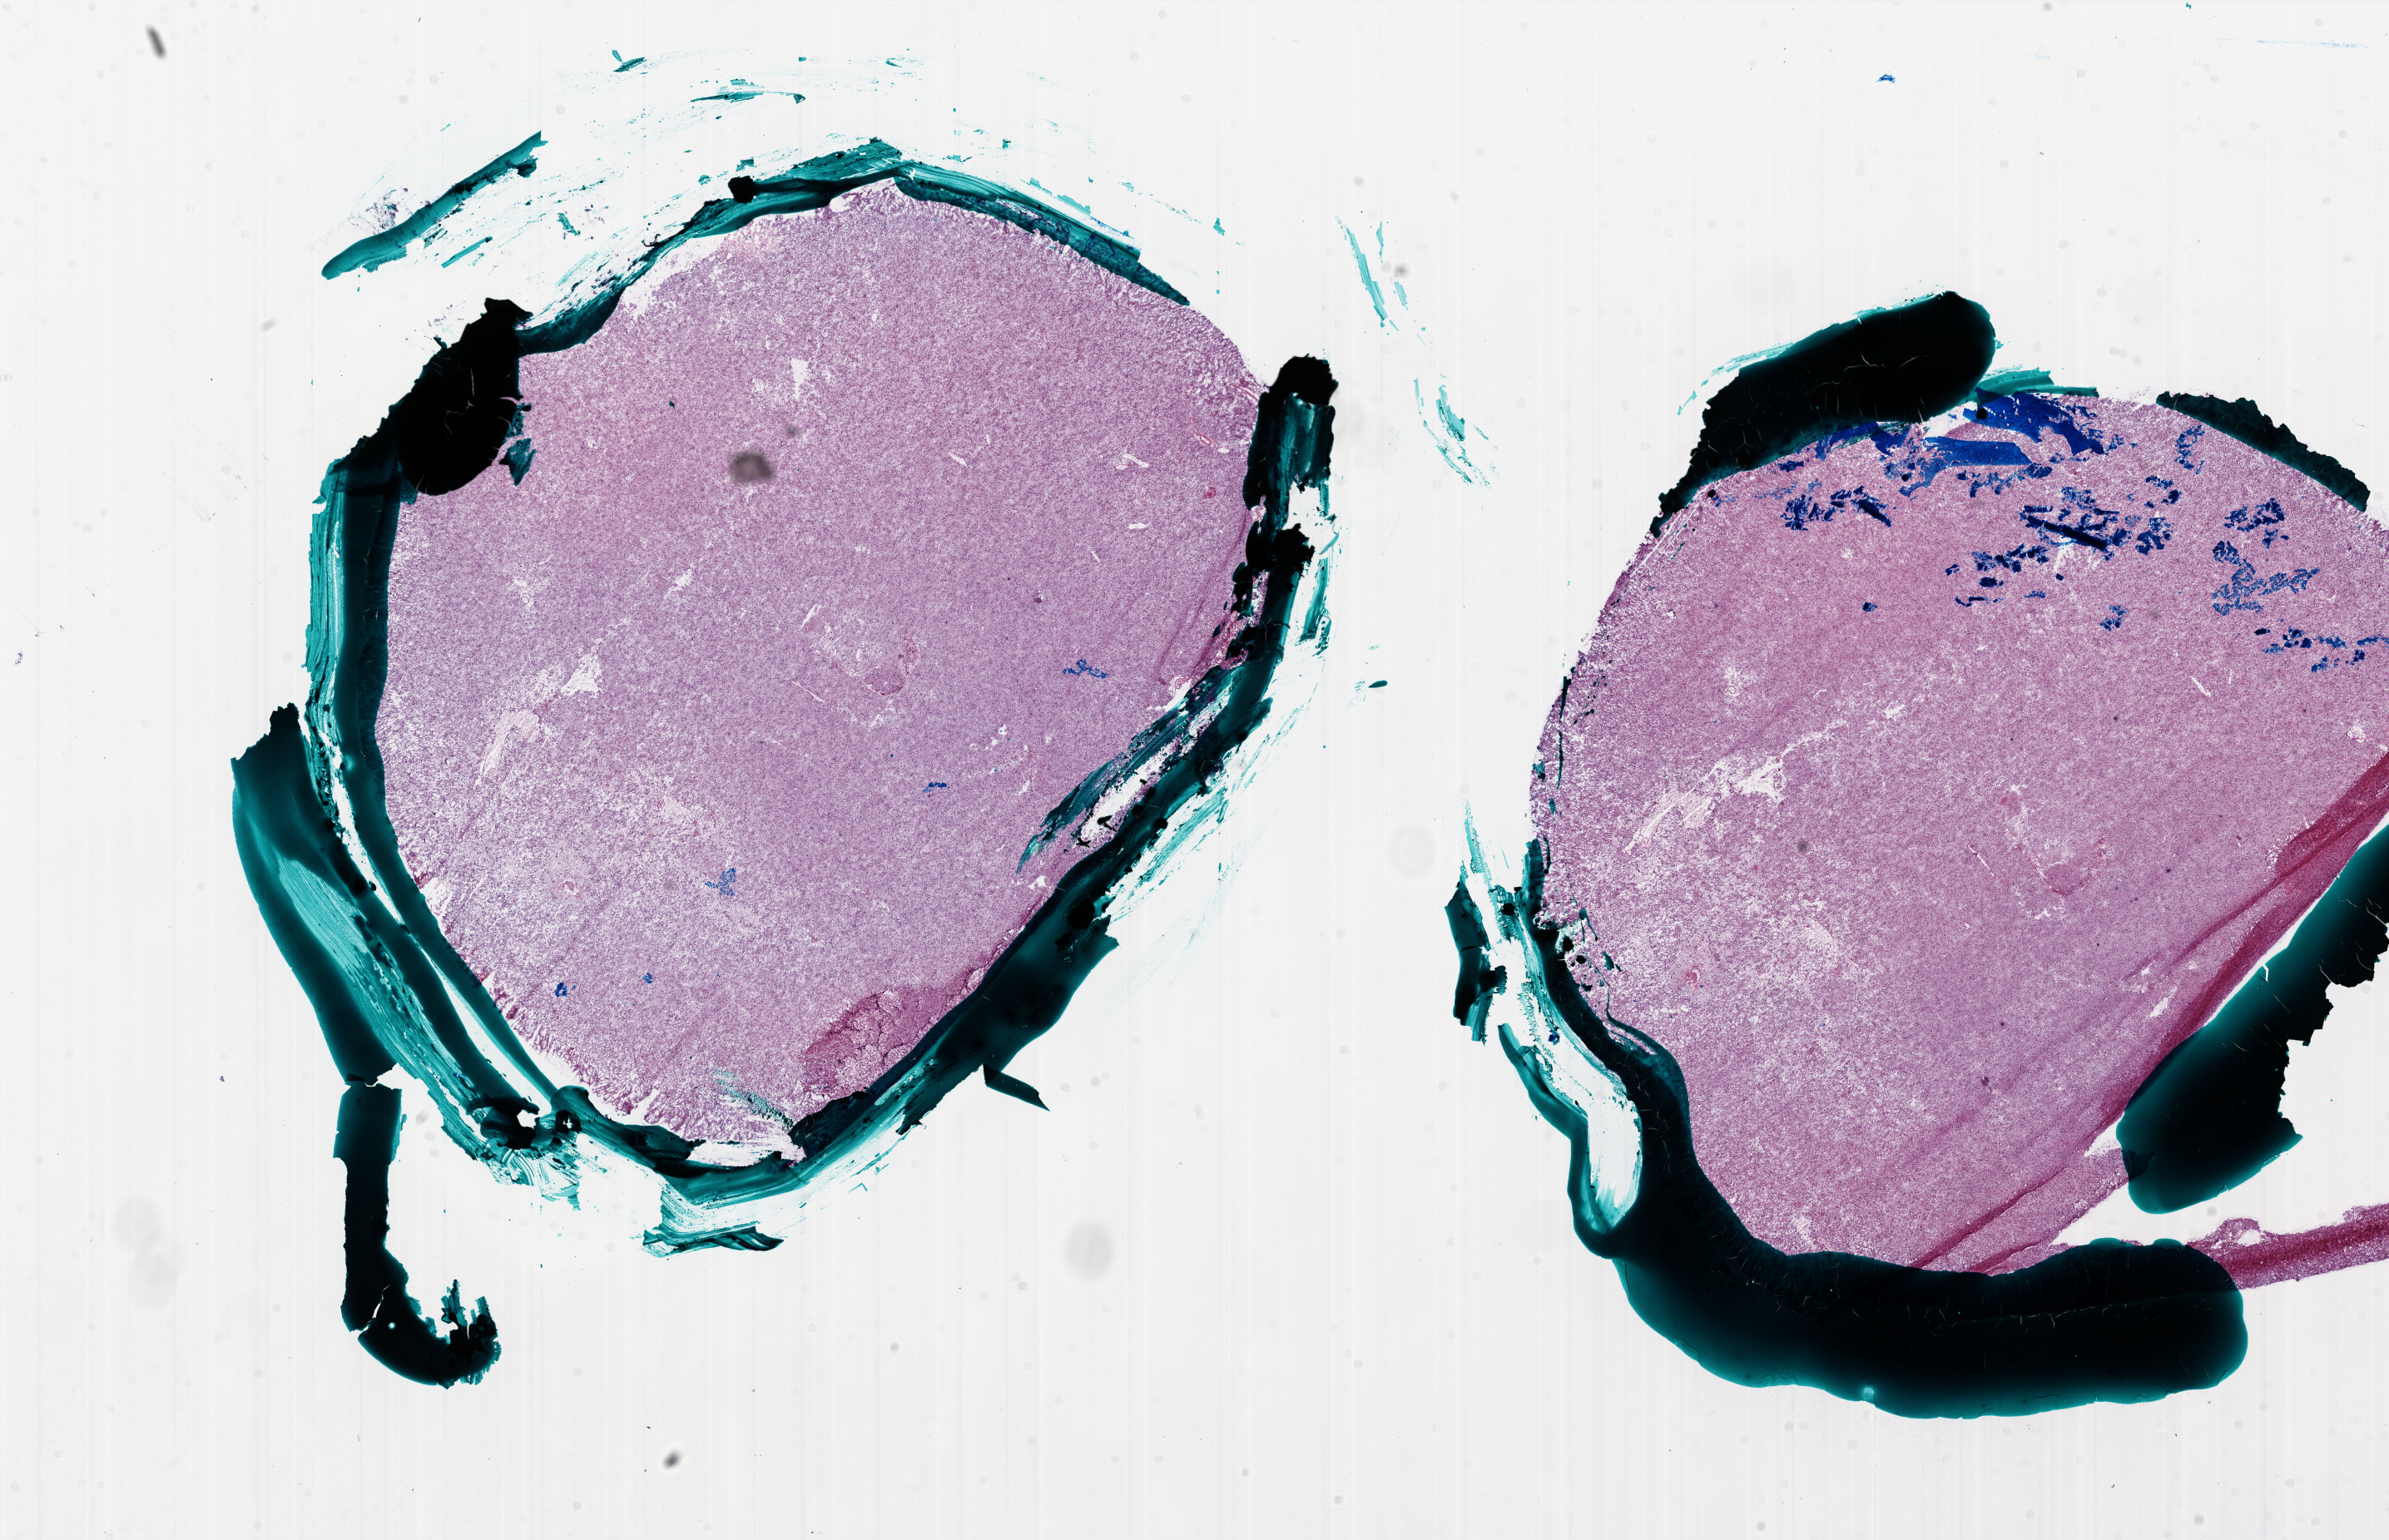
Whole-slide histology image, Hematoxylin and eosin (H&E) stained — low-resolution overview of the scanned area, about 23.0 x 14.8 mm, frozen section from the bottom of the tissue portion, primary tumour sample from the brain. Female patient; age at initial diagnosis 52 years. Pathologist review of this section (percent, as recorded): tumour cells 95%, tumour nuclei 100%, normal cells 0%, stromal cells 0%, necrosis 5%.
Pathologic diagnosis: Glioblastoma.